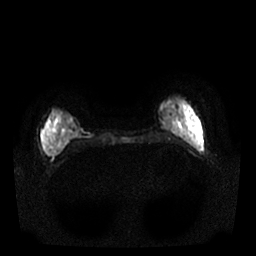
Breast MRI, one axial slice. Slice 6 of 25 in the series (ordered by position). Diffusion-weighted series; image 2 of 4 stored at this slice position (different b-values; order by instance number). 1.5 T. 256 × 256 image matrix, field of view 340 × 340 mm. Female patient.
Annotated regions visible in this slice (manually delineated by an expert):
- tumour on diffusion-weighted imaging: box from (x=45, y=120) to (x=52, y=157) px